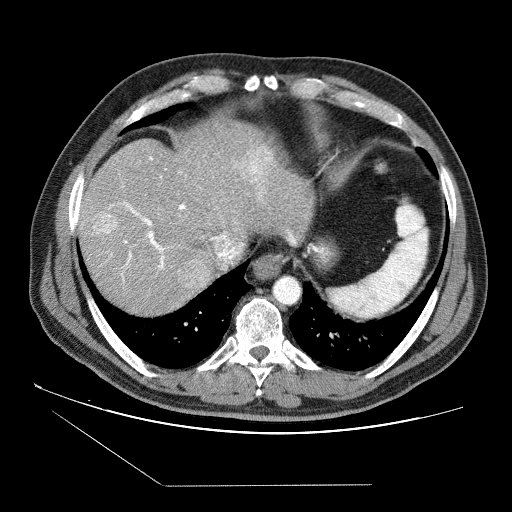
Contrast-enhanced abdominal CT (liver protocol), one axial slice; slice 69 of 87 in the series (ordered by position); reconstruction kernel STANDARD; 120 kVp; soft-tissue window (W 400 / L 40 HU); 512 × 512 image matrix, field of view 400 × 400 mm. Case-level facts recorded for this patient, not image findings: diagnosis: hepatocellular carcinoma (patient treated with transarterial chemoembolisation; whether this scan precedes or follows treatment is not stated here); TNM stage (as recorded): Stage-II; Child-Pugh class: B.
Annotated regions visible in this slice (semi-automatic segmentation, software-assisted and operator-edited):
- abdominal aorta: bounding box [x1, y1, x2, y2] px = [273, 276, 300, 303]
- liver parenchyma outside the tumour (the mass and vessels are separate outlines, so this box may not span the whole liver): [78, 122, 314, 314]
- mass: [93, 147, 271, 289]
- liver vessels: [81, 156, 226, 282]